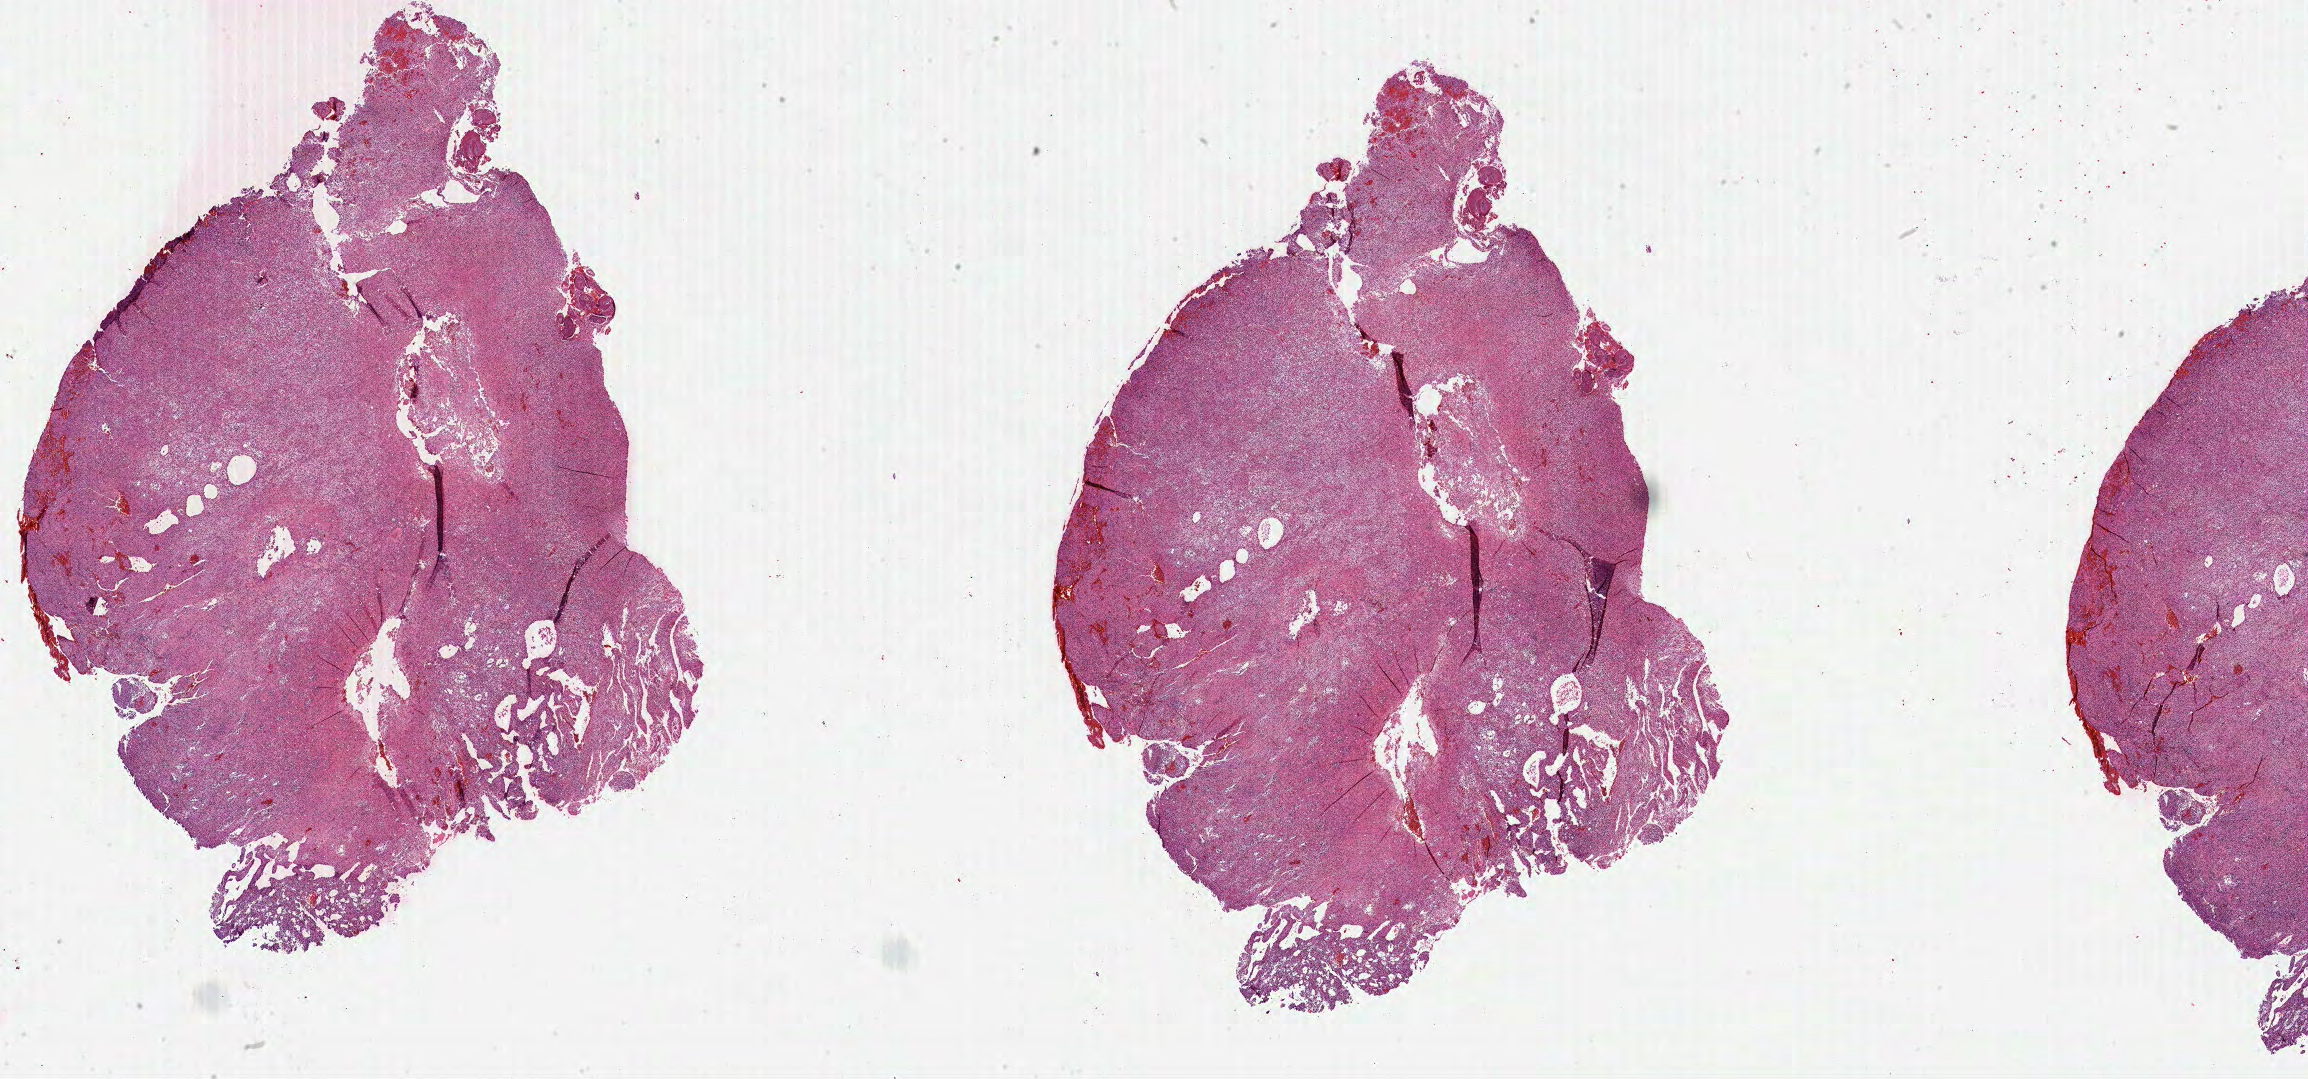
Hematoxylin and eosin (H&E) stained whole-slide image — low-resolution overview of the scanned area, about 37.2 x 17.4 mm, formalin-fixed paraffin-embedded (FFPE) diagnostic section, primary tumour sample from the brain. Male patient; age at initial diagnosis 22 years. Histologic grade: G3 (poorly differentiated).
Pathologic diagnosis: Astrocytoma, anaplastic.